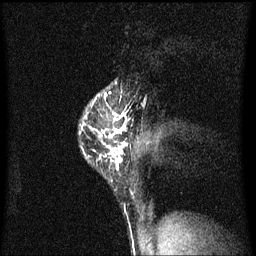
Breast MRI (dynamic contrast-enhanced), one sagittal slice; slice 48 of 60 in the series (ordered by position); dynamic contrast-enhanced series, image 2 of 3 at this slice position (ordered by acquisition); 1.5 T; TE 4.2 ms, TR 8.4 ms; 256 × 256 image matrix, field of view 200 × 200 mm. Patient: female, 40 years.
Structures marked on this image (semi-automatically segmented with operator editing):
- analysis volume of interest (the breast-tissue region the enhancement analysis was run in; not a lesion): bounding box [x1, y1, x2, y2] px = [81, 82, 139, 191]
- tumour enhancement mask (voxels above the 70 % enhancement threshold inside the analysis volume of interest): [94, 92, 128, 171]